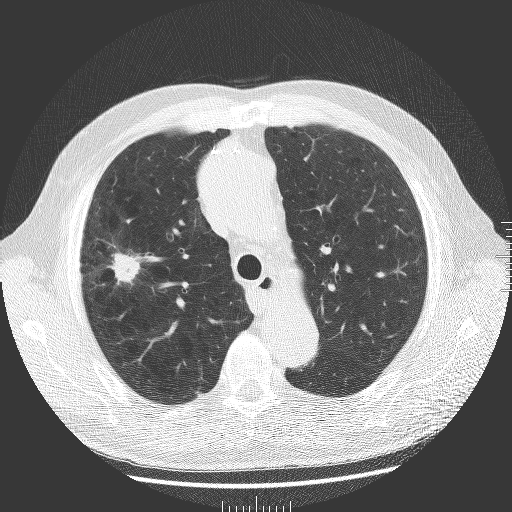
Low-dose screening chest CT, one axial slice; slice 134 of 181 in the series (ordered by position); reconstruction kernel BONE; 120 kVp; lung window (W 1500 / L -600 HU); 512 × 512 image matrix, field of view 380 × 380 mm.
Structures marked on this image (manually delineated by an expert):
- lesion 1 (tumor, upper lobe of right lung): bounding box <110,252,140,284> (left, top, right, bottom; pixels)